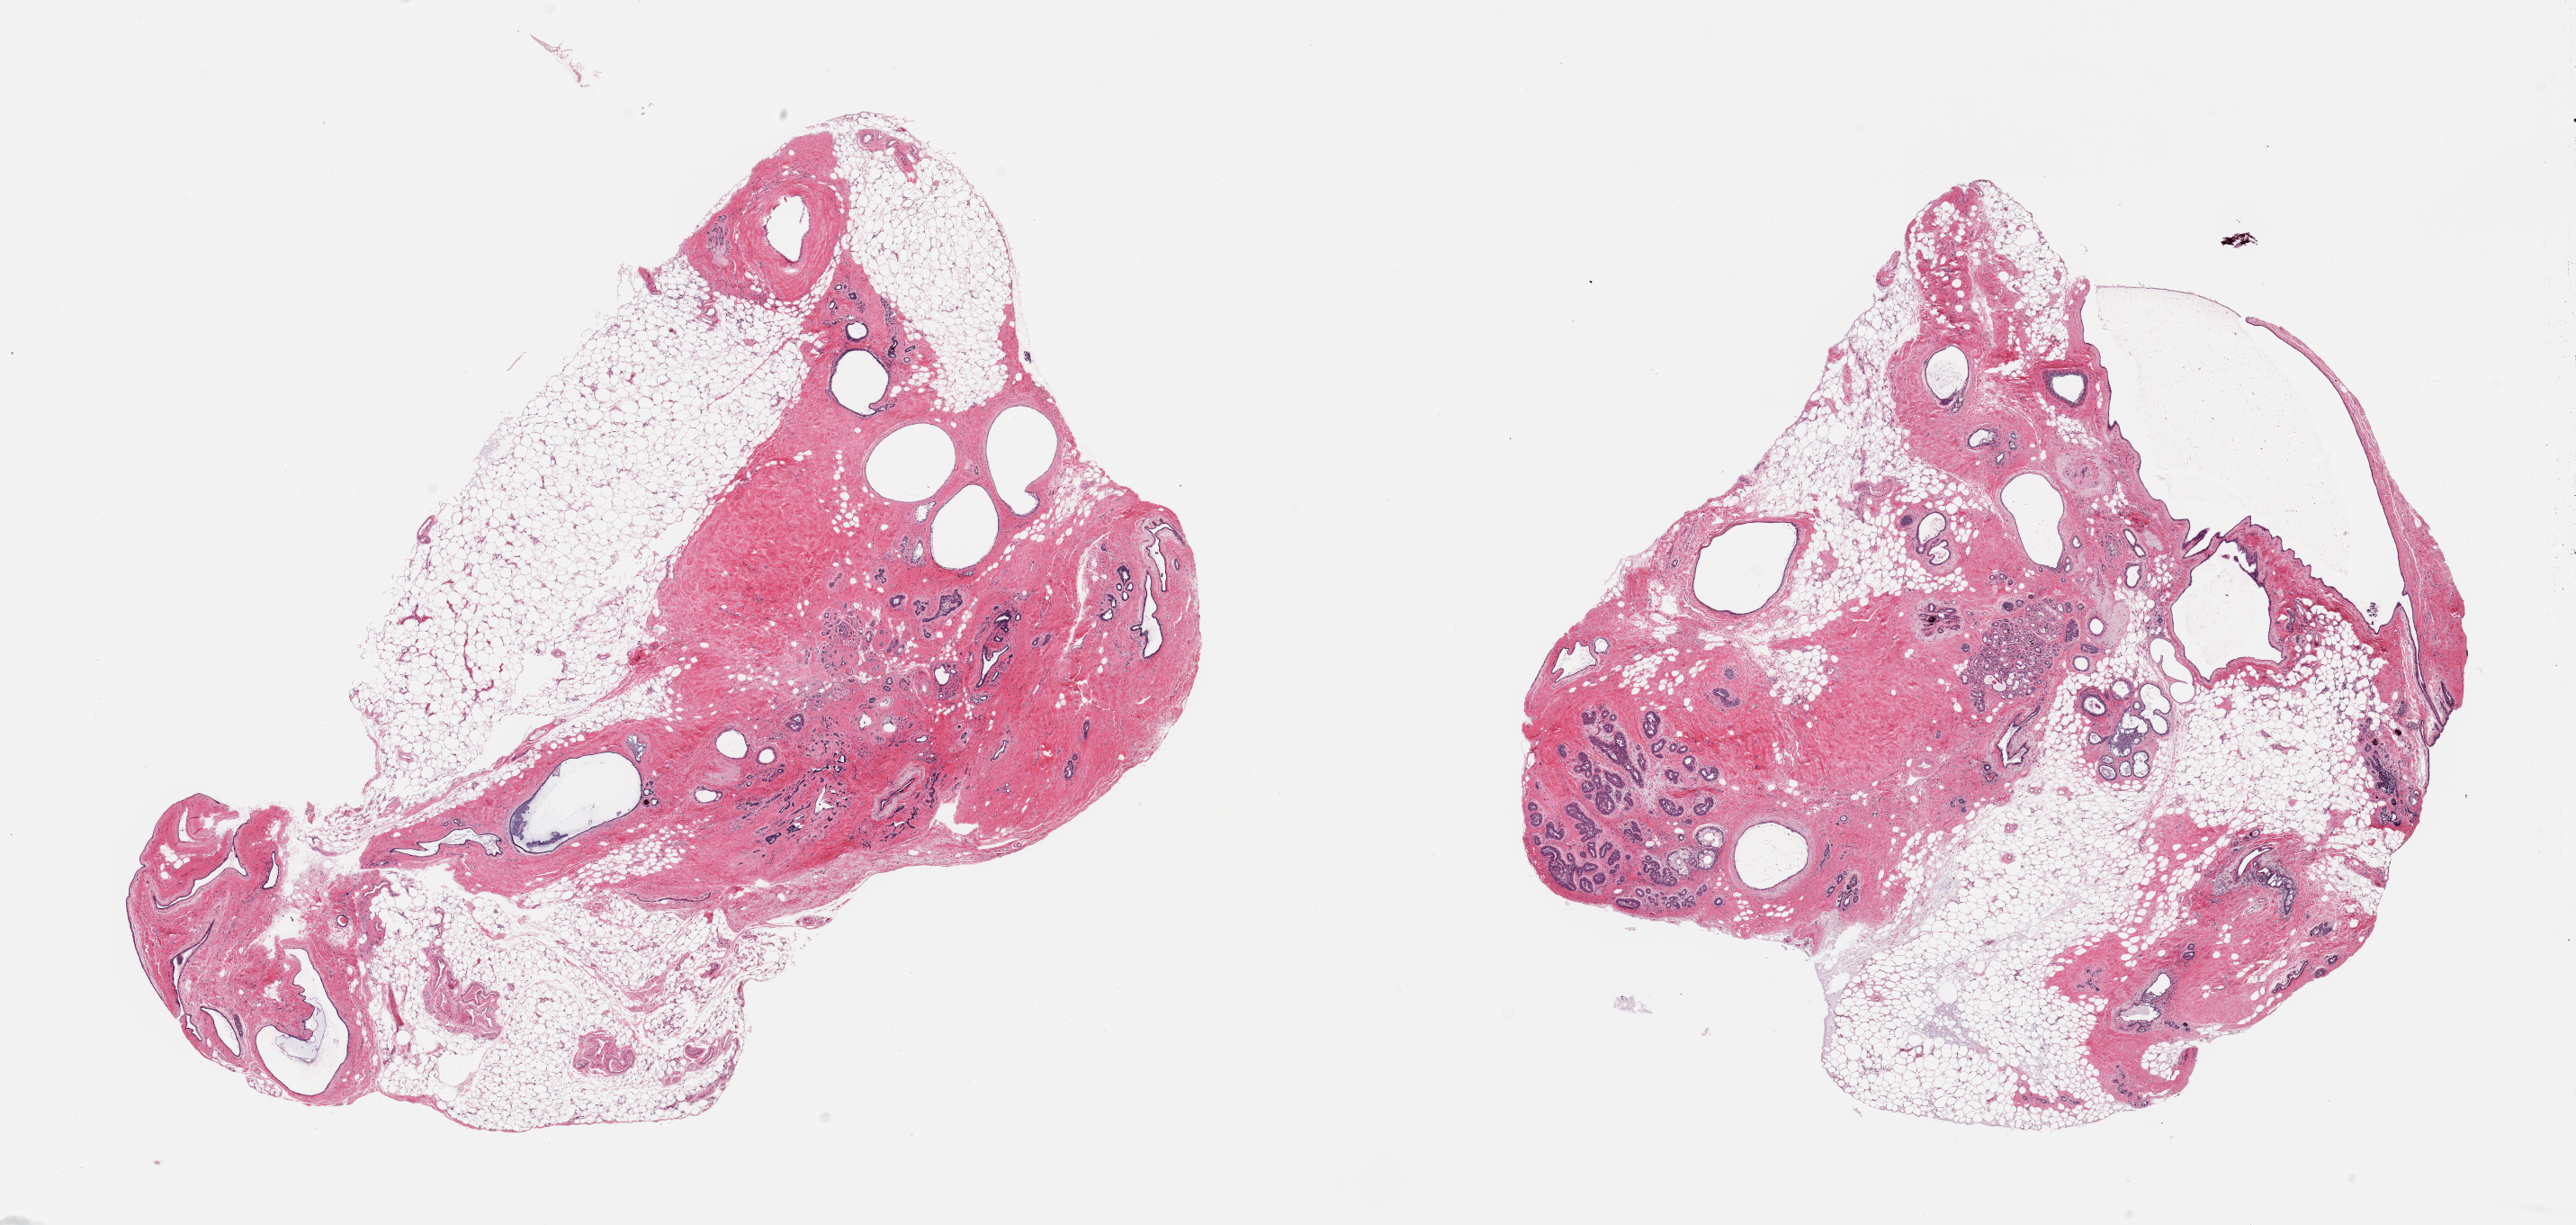
Digitized H&E-stained section, whole scanned area (about 22.6 x 10.8 mm, acquisition: 20x scan) shown as a low-resolution overview. PAXgene-fixed paraffin-embedded (PFPE) section. Target tissue: breast. Tissue donor sample. Donor sex: female.
- reviewer comment on this tissue sample: 2 pieces, fibrocystic changes and duct ectasia present